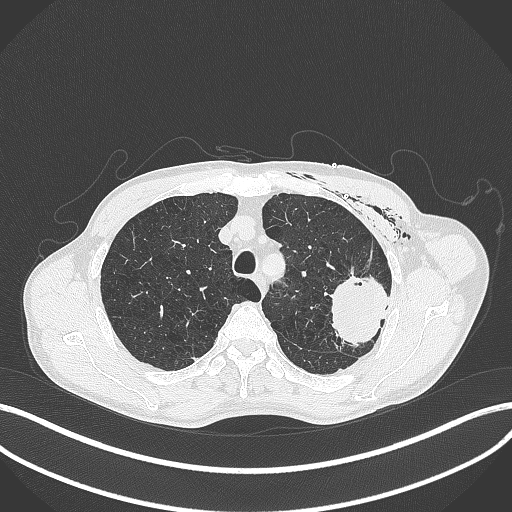
Chest CT, one axial slice; position 318 of 457 along the scan axis; reconstruction kernel B70f; 120 kVp; lung window (W 1500 / L -600 HU); 512 × 512 image matrix, field of view 400 × 400 mm. Male patient, age 58 years. From the clinical record (not read from this slice): clinical TNM (as recorded): T3 N0 M0.
Structures marked on this image (rectangle marked by the reading radiologist):
- lung tumour (recorded histology: adenocarcinoma): bounding box (x1, y1, x2, y2) in pixels: (323, 268, 392, 350)